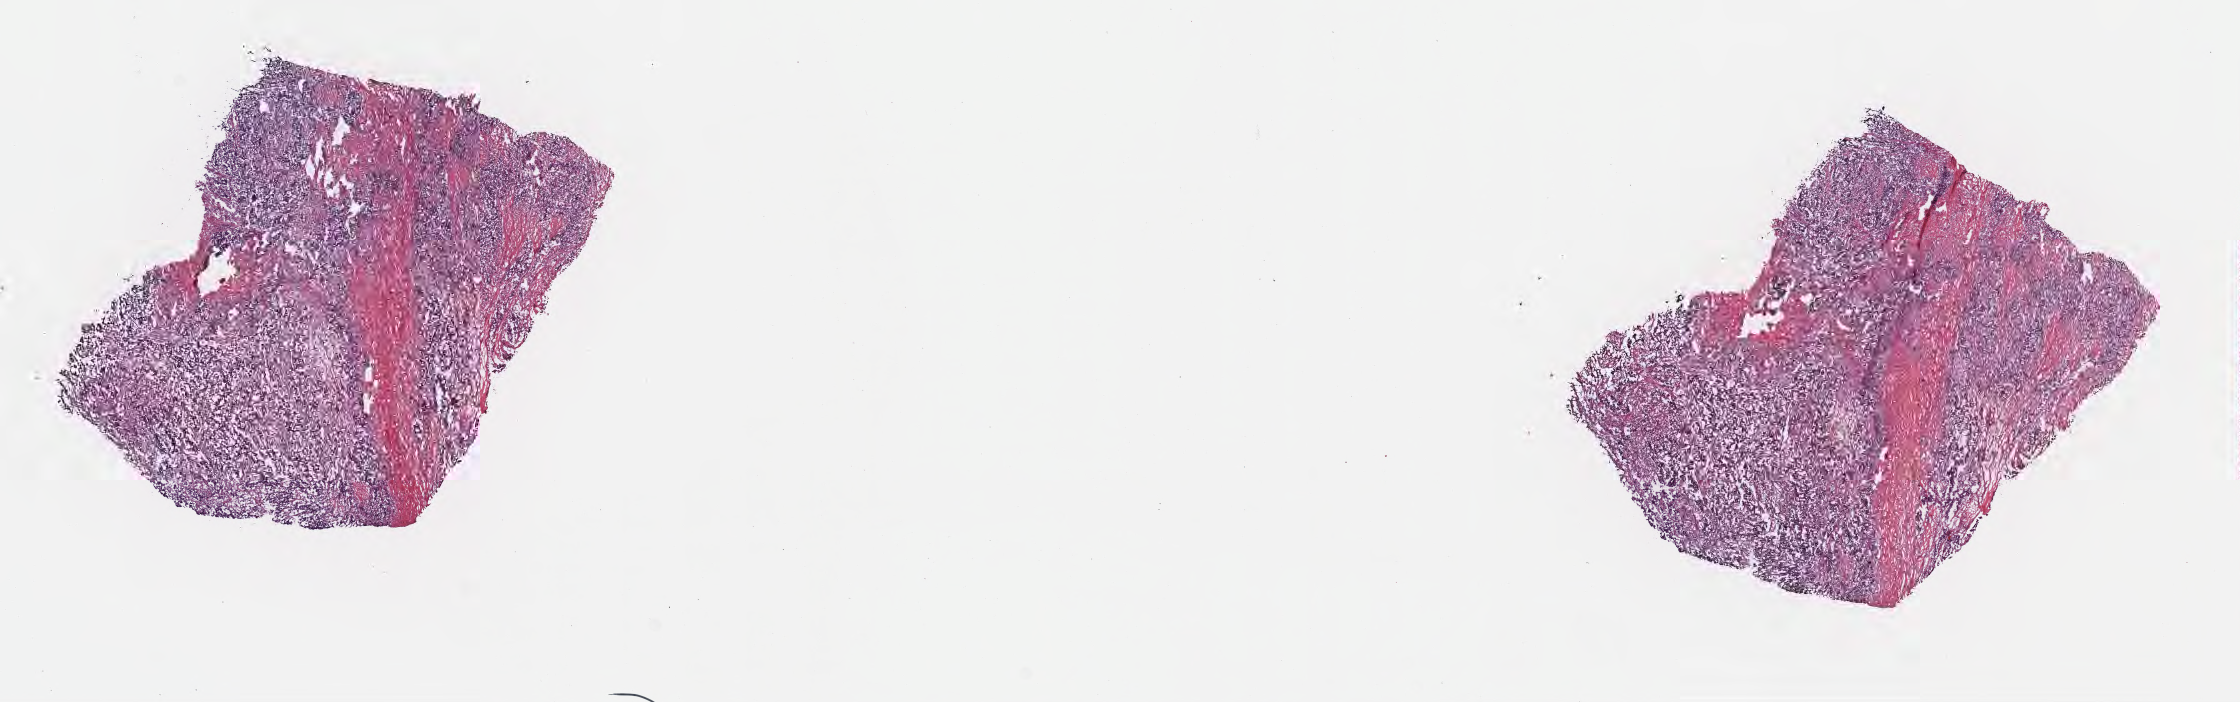
Haematoxylin and eosin whole-slide image — a low-resolution overview of the entire scanned area, about 18.1 x 5.7 mm; cryosection; specimen: primary tumor; anatomic site: upper lobe of right lung. Patient: male, age 57 years. Pathologist review of this section (percent, as recorded): tumor cells 70%, tumor nuclei 75%, stromal cells 20%, necrosis 0%, normal cells 10%. Inflammatory infiltration, as recorded: lymphocyte infiltration 5%, monocyte infiltration 5%, neutrophil infiltration 0%.
Diagnosis: Adenocarcinoma, NOS. Section: top of the tissue portion. AJCC pathologic stage: Stage IIB.